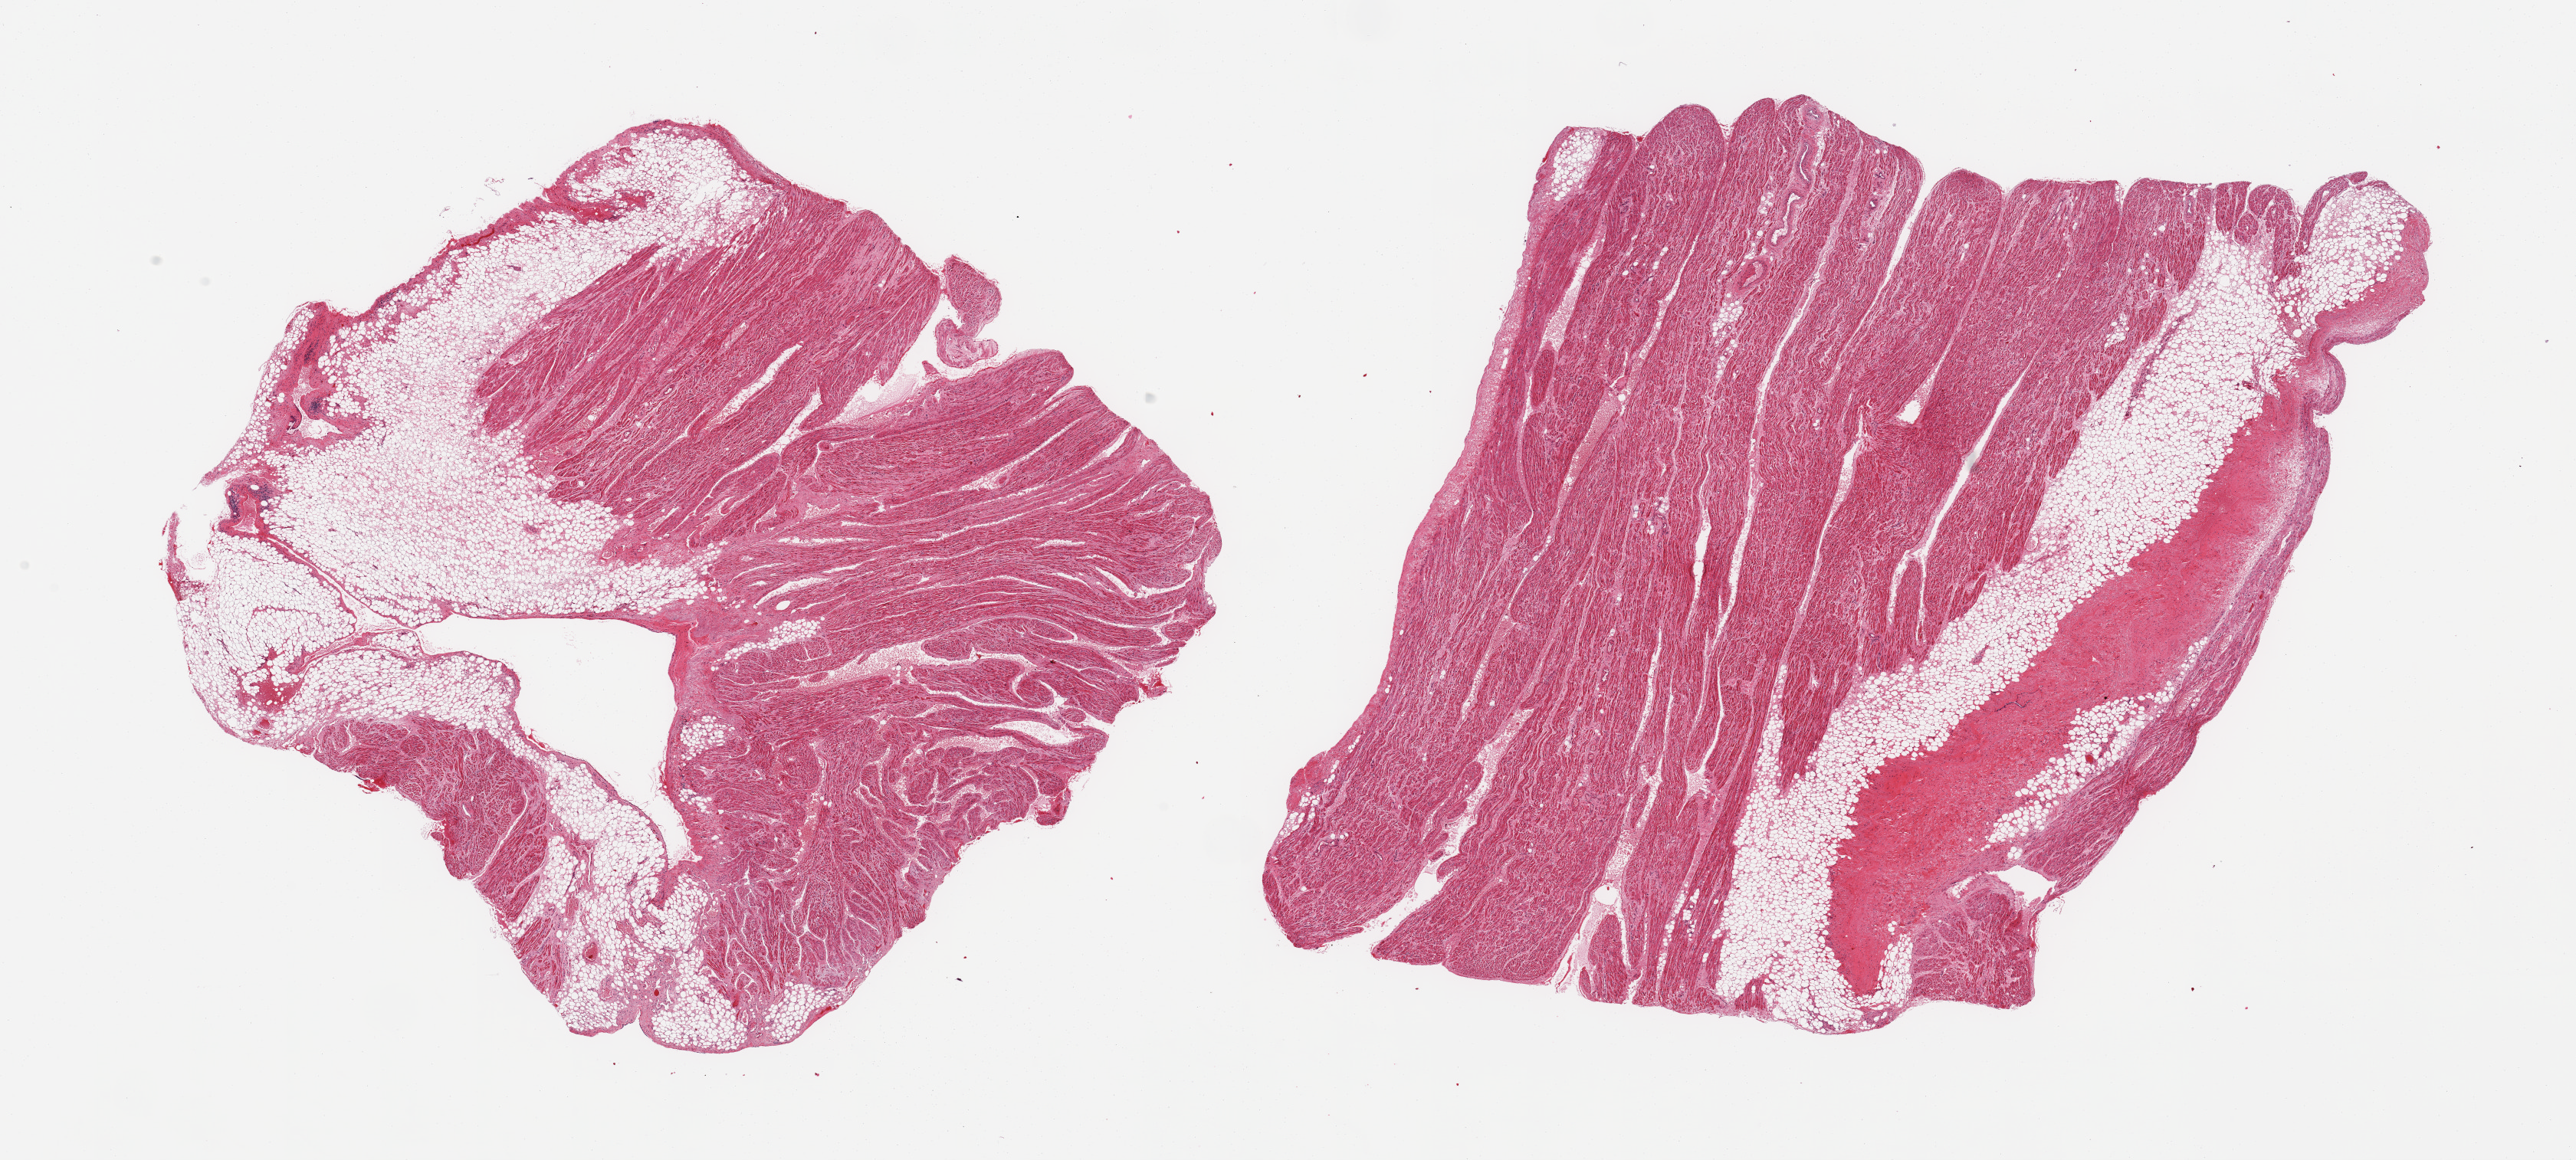
Haematoxylin and eosin whole-slide image, low-resolution overview of the scanned area, about 26.6 x 12.0 mm (from a 20x scan). PAXgene-fixed, paraffin-embedded tissue. Target tissue: auricular appendage. Donor tissue sample. Male donor.
Reviewer comment on this tissue sample: 2 pieces, no abnormalities.